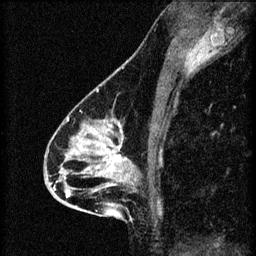
Breast MRI (dynamic contrast-enhanced), one sagittal slice. Slice 36 of 60 in the series (ordered by position). 3 images stored at this slice position (order not interpretable as contrast timing). 1.5 T. TE 4.2 ms, TR 8.2 ms. 256 × 256 image matrix. Female patient, age 46 years.
Structures marked on this image (semi-automatically segmented with operator editing):
- analysis volume of interest (the breast-tissue region the enhancement analysis was run in; not a lesion): bounding box <55,114,141,209> (left, top, right, bottom; pixels)
- tumour enhancement mask (voxels above the 70 % enhancement threshold inside the analysis volume of interest): <65,118,129,199>